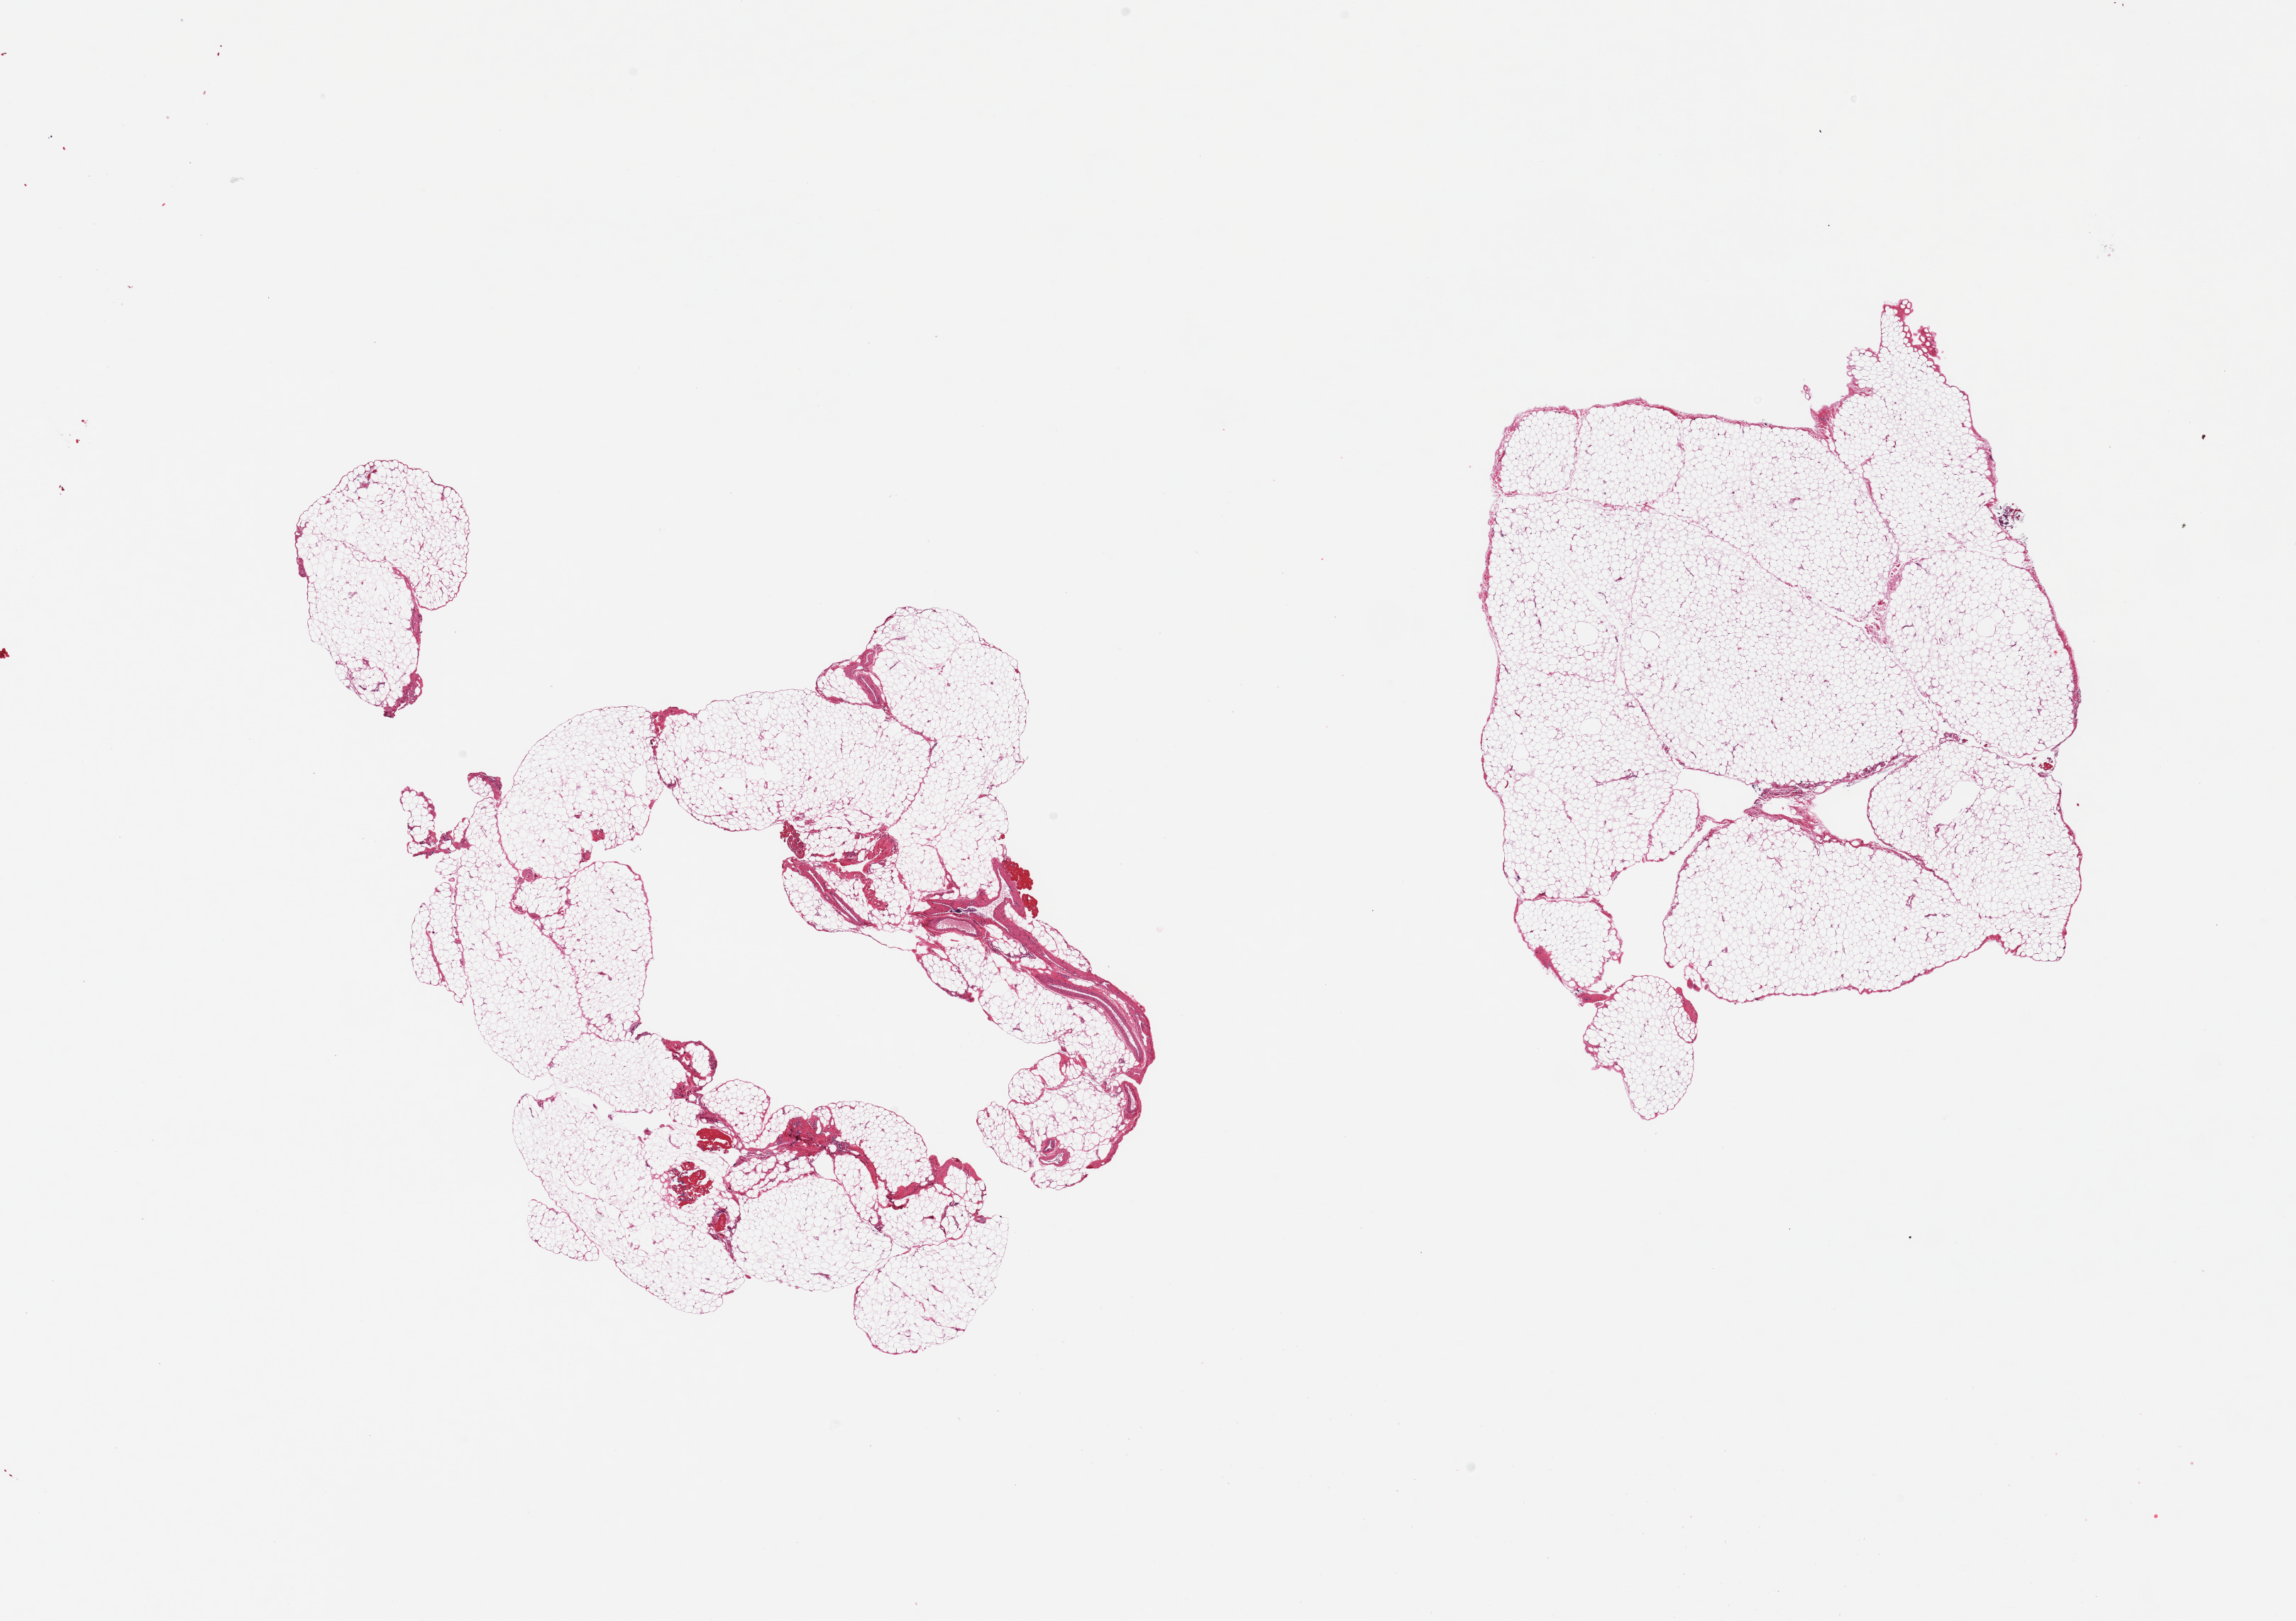
Whole-slide image, haematoxylin and eosin stain, a low-resolution overview of the entire scanned area, about 25.6 x 18.1 mm (acquisition: 20x scan); PAXgene-fixed paraffin-embedded (PFPE) section; sampled site (target tissue): omentum; tissue donor sample.
- review note (as recorded): 2 pieces, ~10% fascia/mesothelial/vascular elements